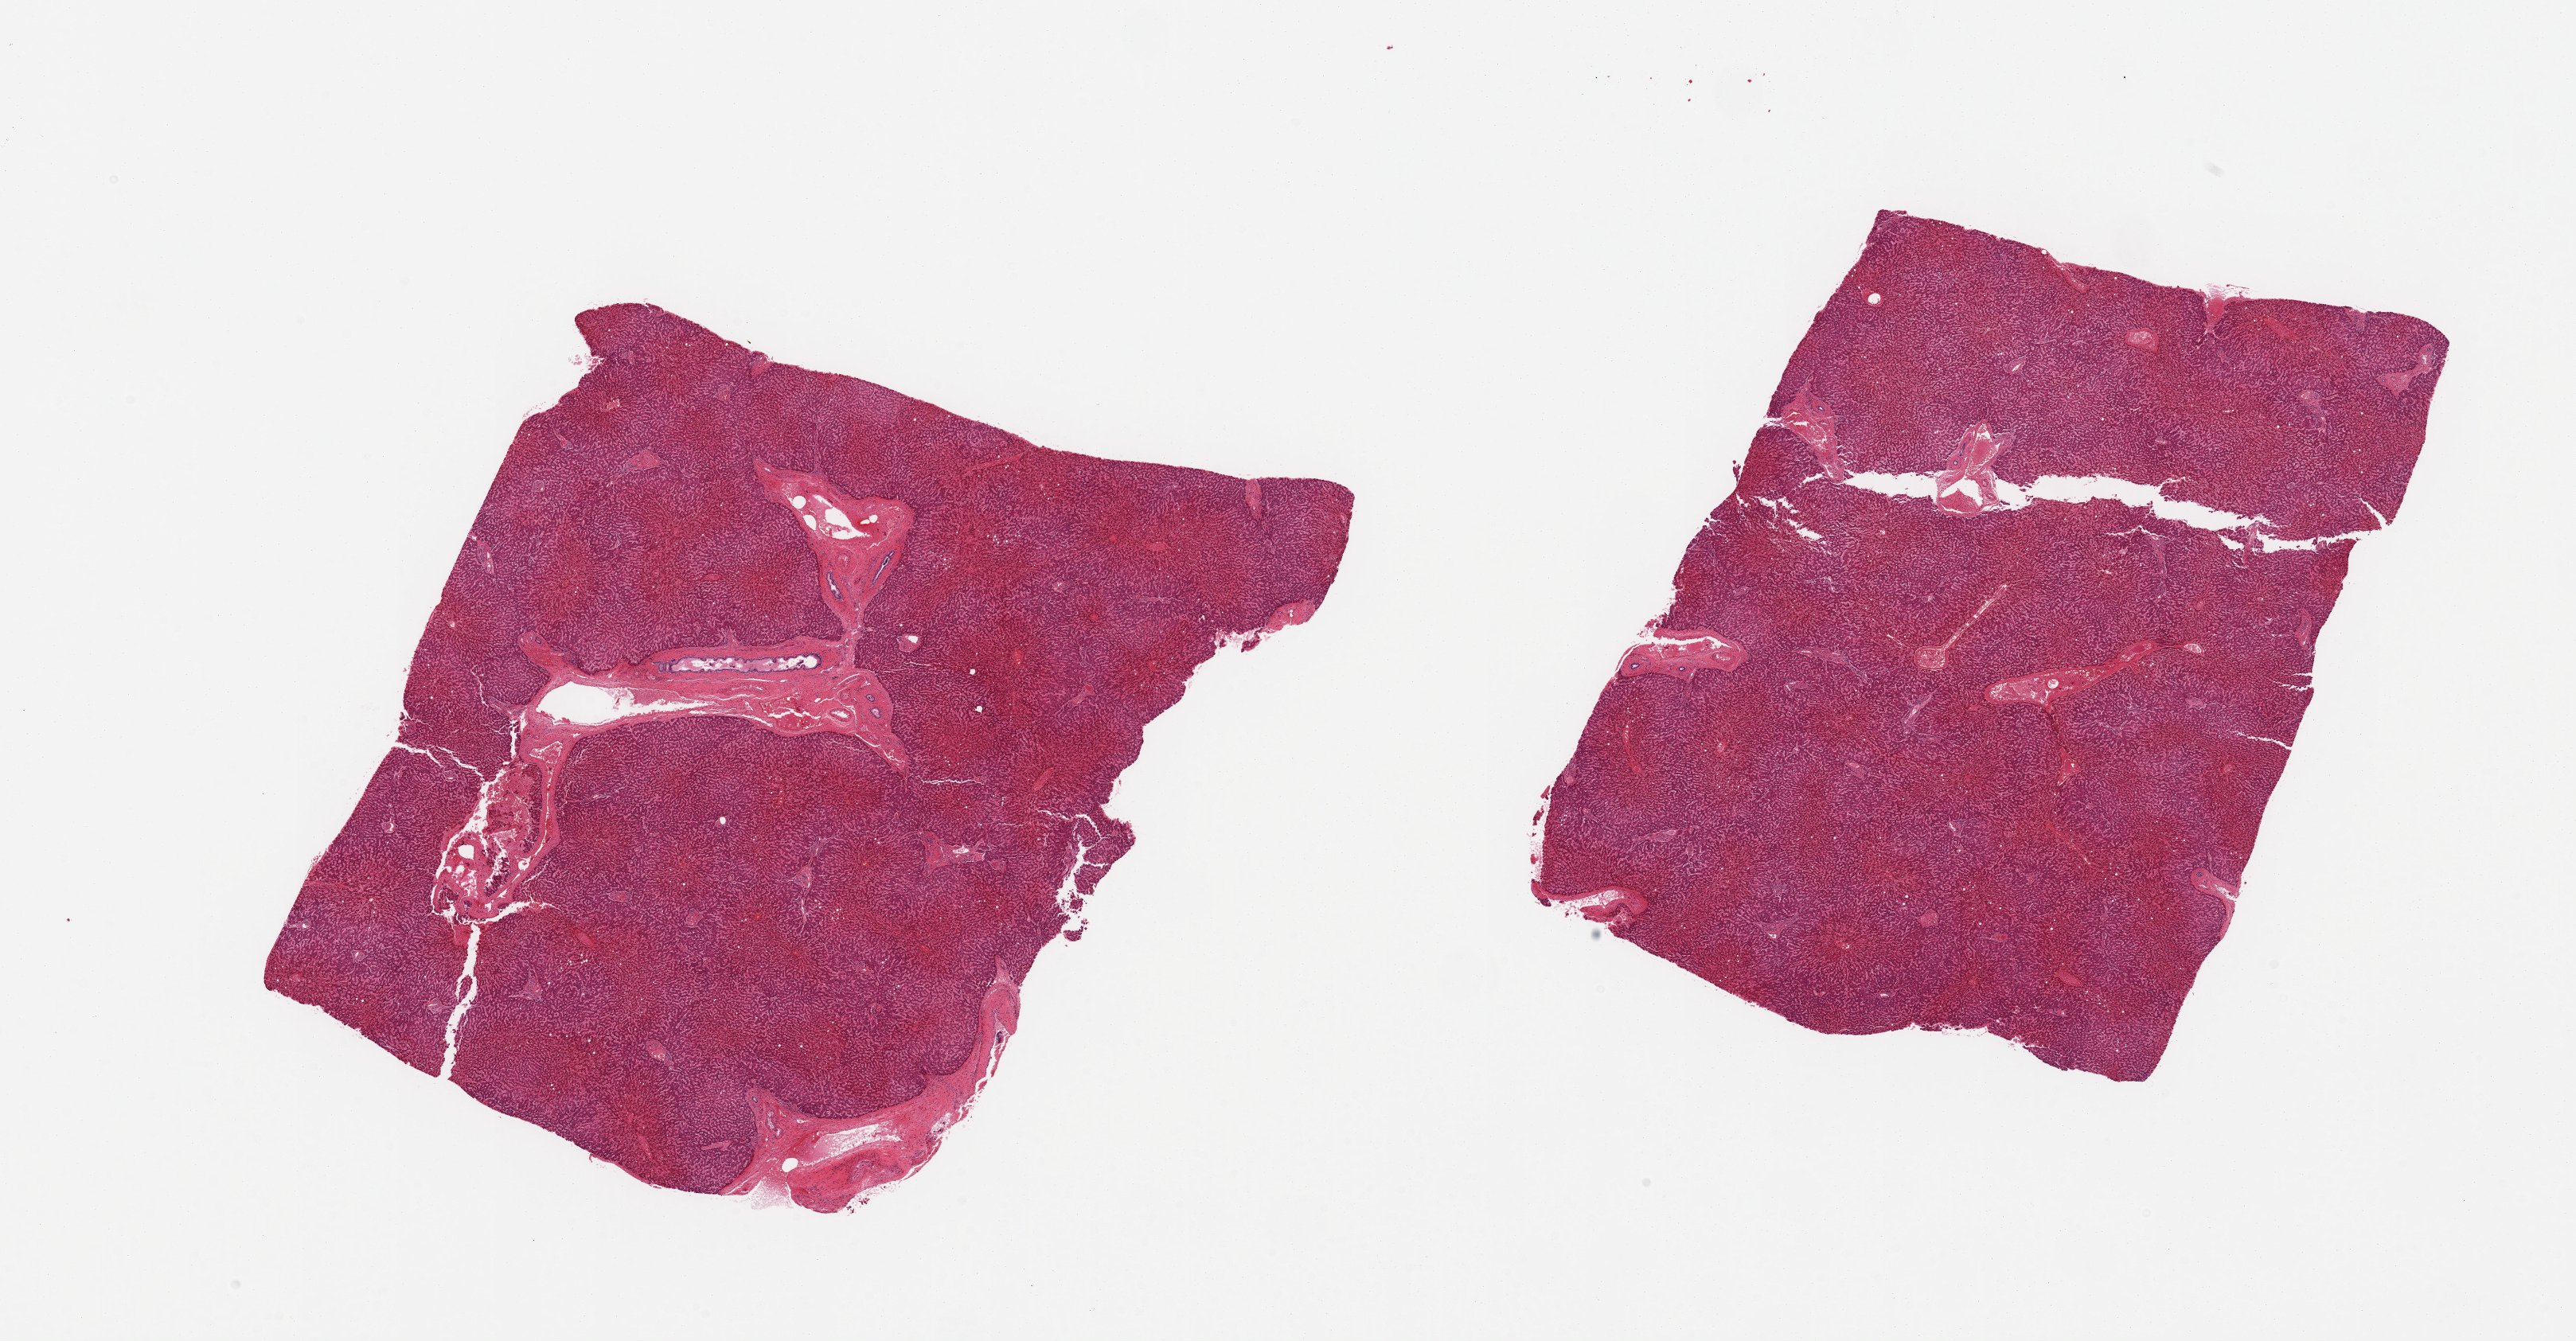
Haematoxylin and eosin whole-slide image, a low-resolution overview of the entire scanned area, about 25.6 x 13.3 mm (slide scanned at 20x). PAXgene-fixed, paraffin-embedded tissue. Section of liver (target tissue). Donor tissue sample.
- reviewer comment on this tissue sample: 2 pieces, moderate/focally marked passive congestion, cardiac features